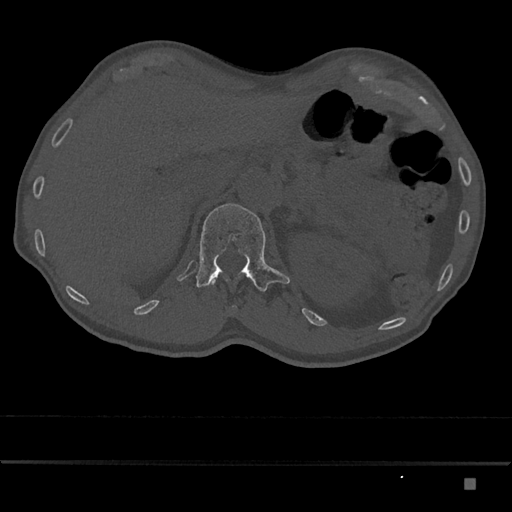
CT including the spine, one axial slice. Slice 559 of 797 in the series (ordered by position). Reconstruction kernel Br40s/3. 120 kVp. Bone window (W 1800 / L 400 HU). 0.5 mm slice thickness. 512 × 512 image matrix. Patient: male, 72 years. Case-level facts recorded for this patient, not image findings: primary cancer: prostate.
Structures marked on this image (semi-automatically segmented with operator editing):
- L1 vertebra: box from (x=196, y=203) to (x=290, y=291) px
- T12 vertebra: (x=209, y=278)–(x=228, y=285)